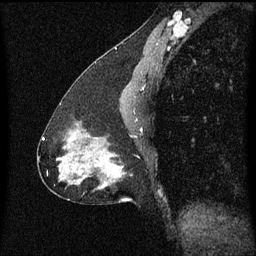
Breast MRI (dynamic contrast-enhanced), one sagittal slice; dynamic contrast-enhanced series, image 2 of 3 at this slice position (ordered by acquisition); 1.5 T; TE 4.2 ms, TR 8.4 ms; 2 mm slice thickness; 256 × 256 image matrix. Patient: female, 47 years.
Structures marked on this image (semi-automatic segmentation, software-assisted and operator-edited):
- analysis volume of interest (the breast-tissue region the enhancement analysis was run in; not a lesion): bounding box (x1, y1, x2, y2) in pixels: (81, 140, 132, 189)
- tumour enhancement mask (voxels above the 70 % enhancement threshold inside the analysis volume of interest): (111, 164, 119, 175)